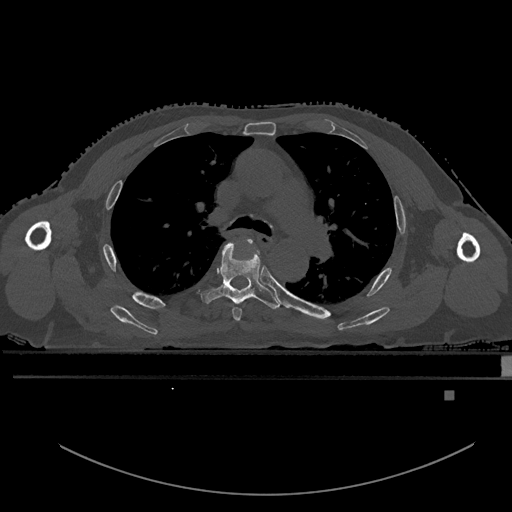
CT including the spine, one axial slice; slice 368 of 969 in the series (ordered by position); bone window (W 1800 / L 400 HU); 0.5 mm slice thickness; 512 × 512 image matrix. Patient: male, 82 years. Case-level facts recorded for this patient, not image findings: primary cancer: prostate; vertebrae with lytic lesions (as recorded): T11, T9, T8, T2.
Structures marked on this image (semi-automatically segmented with operator editing):
- T4 vertebra: bounding box <233,237,253,321> (left, top, right, bottom; pixels)
- T5 vertebra: <201,241,280,310>